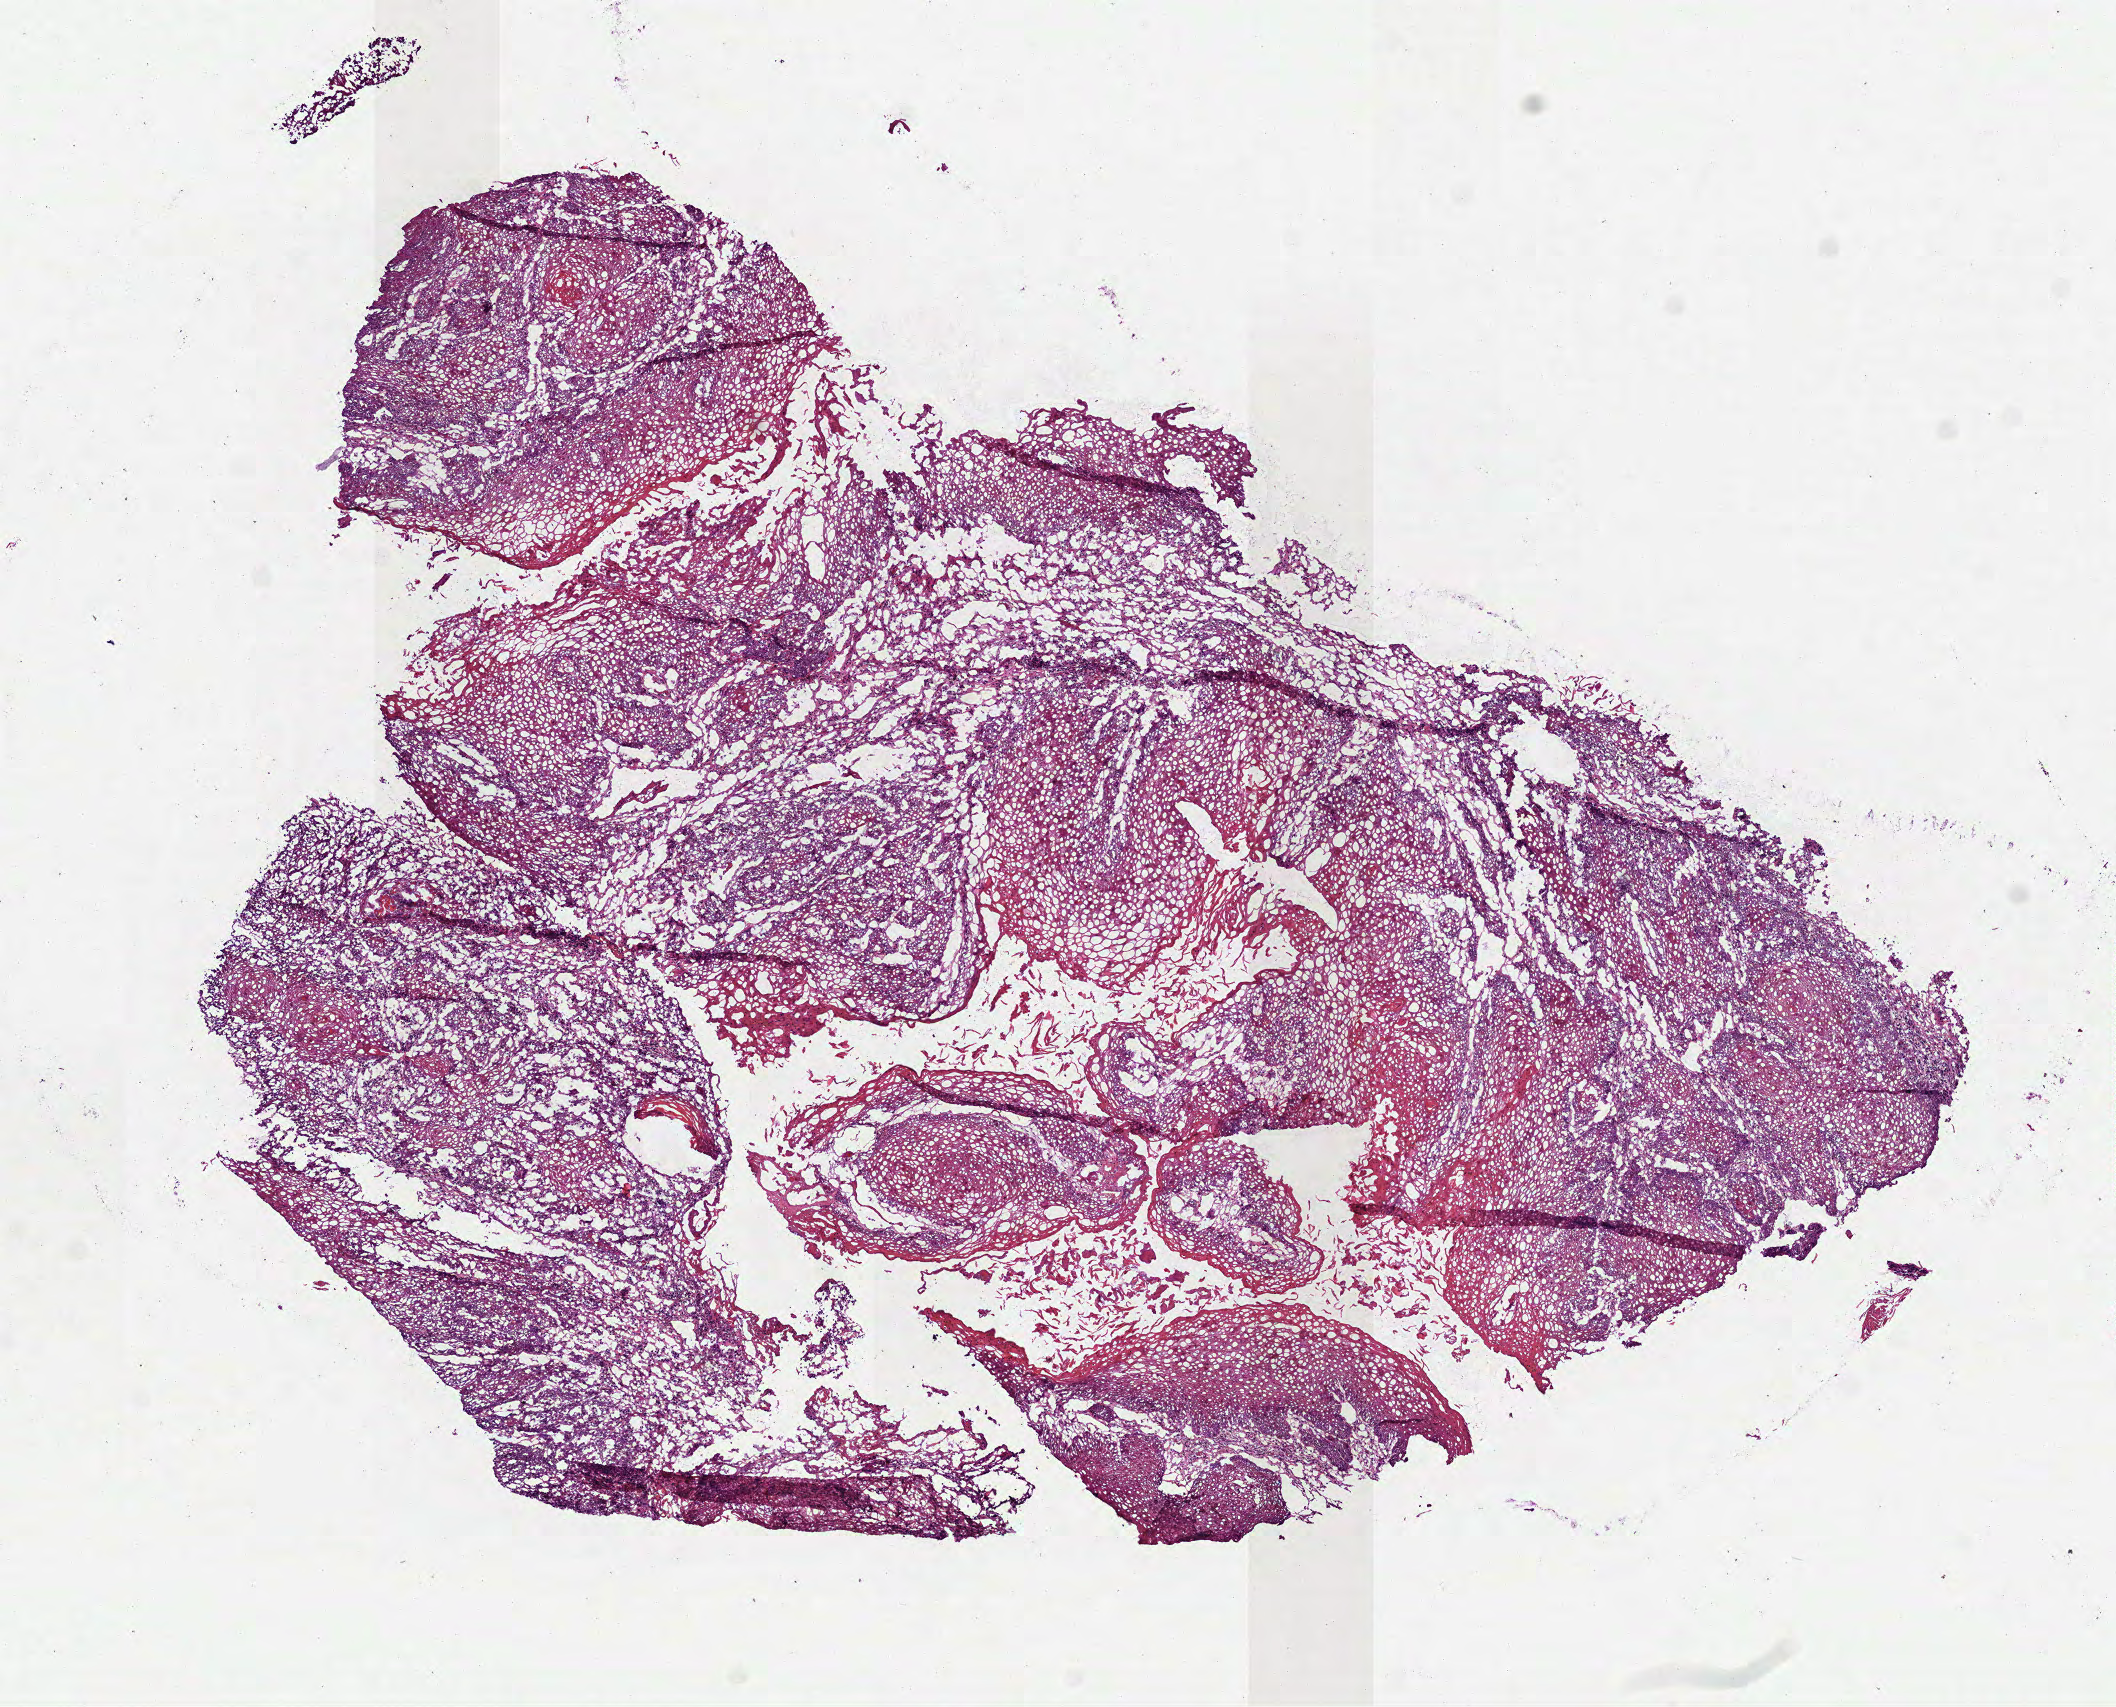
H&E-stained whole-slide image, low-resolution overview of the scanned area, about 8.5 x 6.9 mm (from a 40x scan), frozen section from the bottom of the tissue portion, sample: primary tumour, head and neck. Patient: male, age at initial diagnosis 62 years. Histologic grade: G1 (well differentiated). Slide review estimates, as recorded: tumour cells 90%, tumour nuclei 85%, normal cells 0%, stromal cells 10%, necrosis 0%.
* diagnosis: Squamous cell carcinoma, NOS (tongue, NOS)
* AJCC pathologic stage: IVA (7th edition)